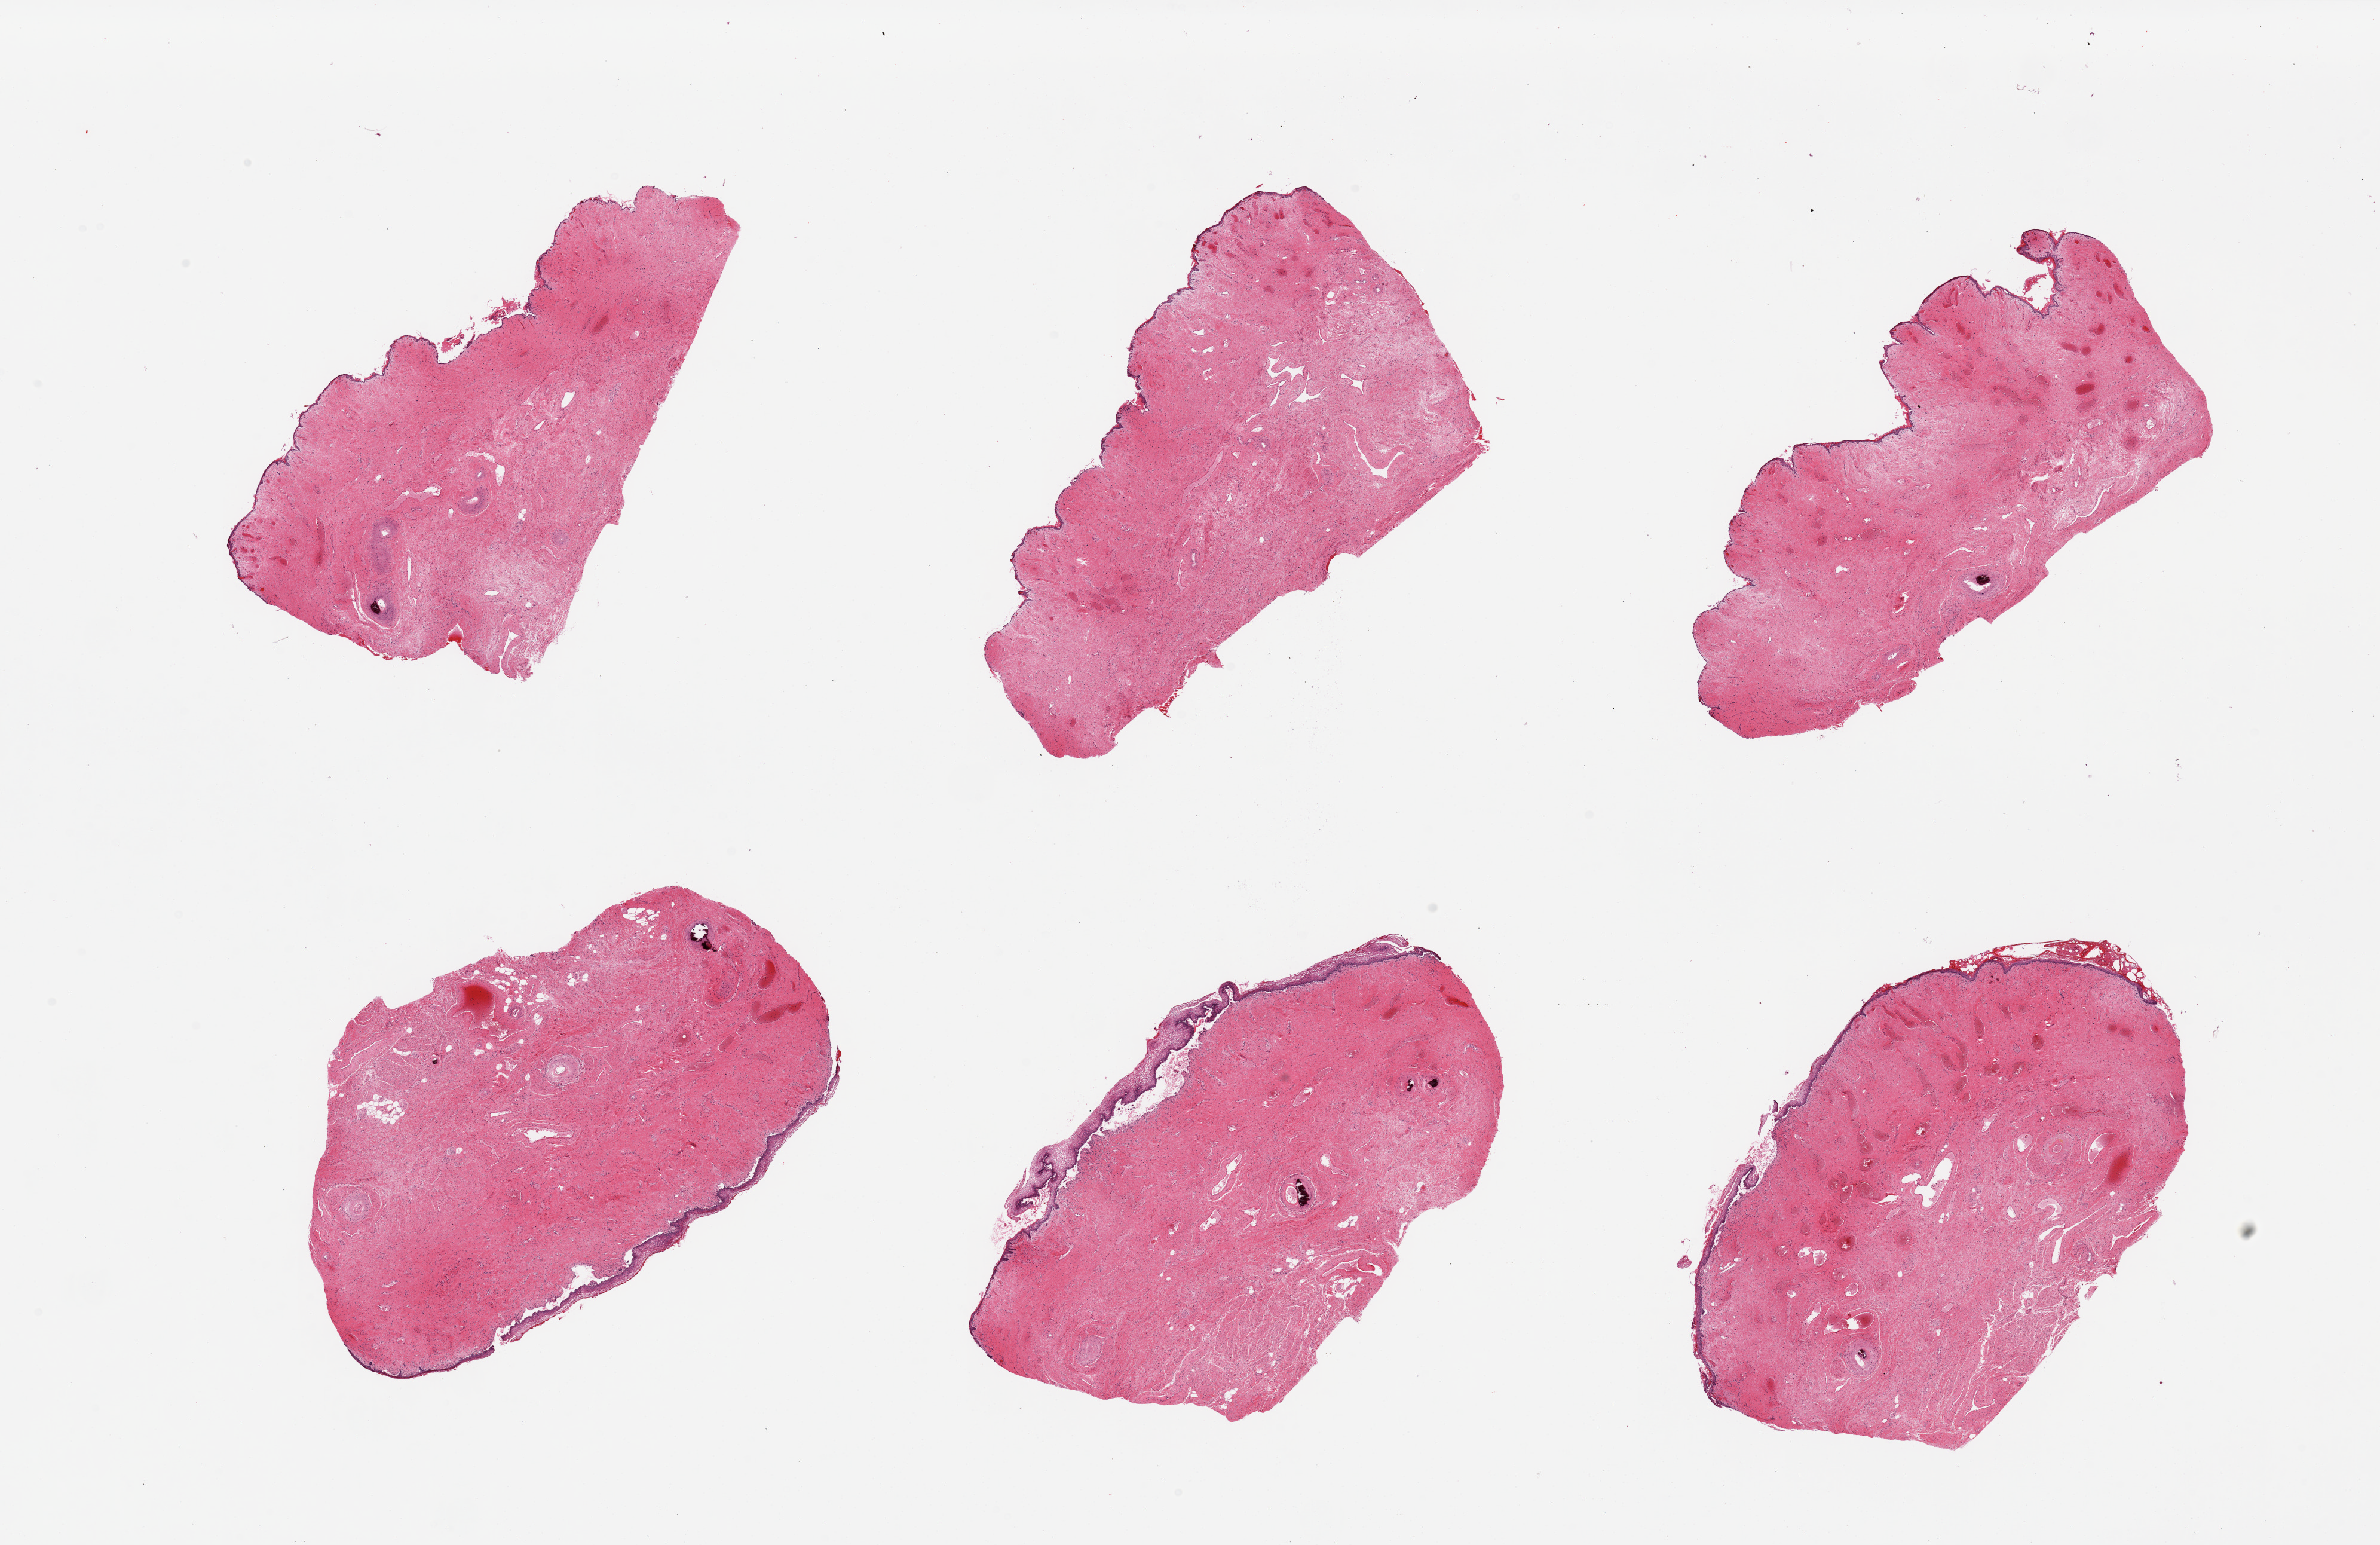
Digitized haematoxylin and eosin-stained section, brightfield — shown as a low-resolution overview of the whole scanned area (about 31.5 x 20.4 mm, slide scanned at 20x). PAXgene-fixed, paraffin-embedded tissue. Target tissue: vagina. Donor tissue sample. Female donor.
Pathologist's review note for this sample: 6 pieces, squamous epithelium is largely sloughed in several pieces, arteriosclerosis with calcification and narrowing of the lumen.